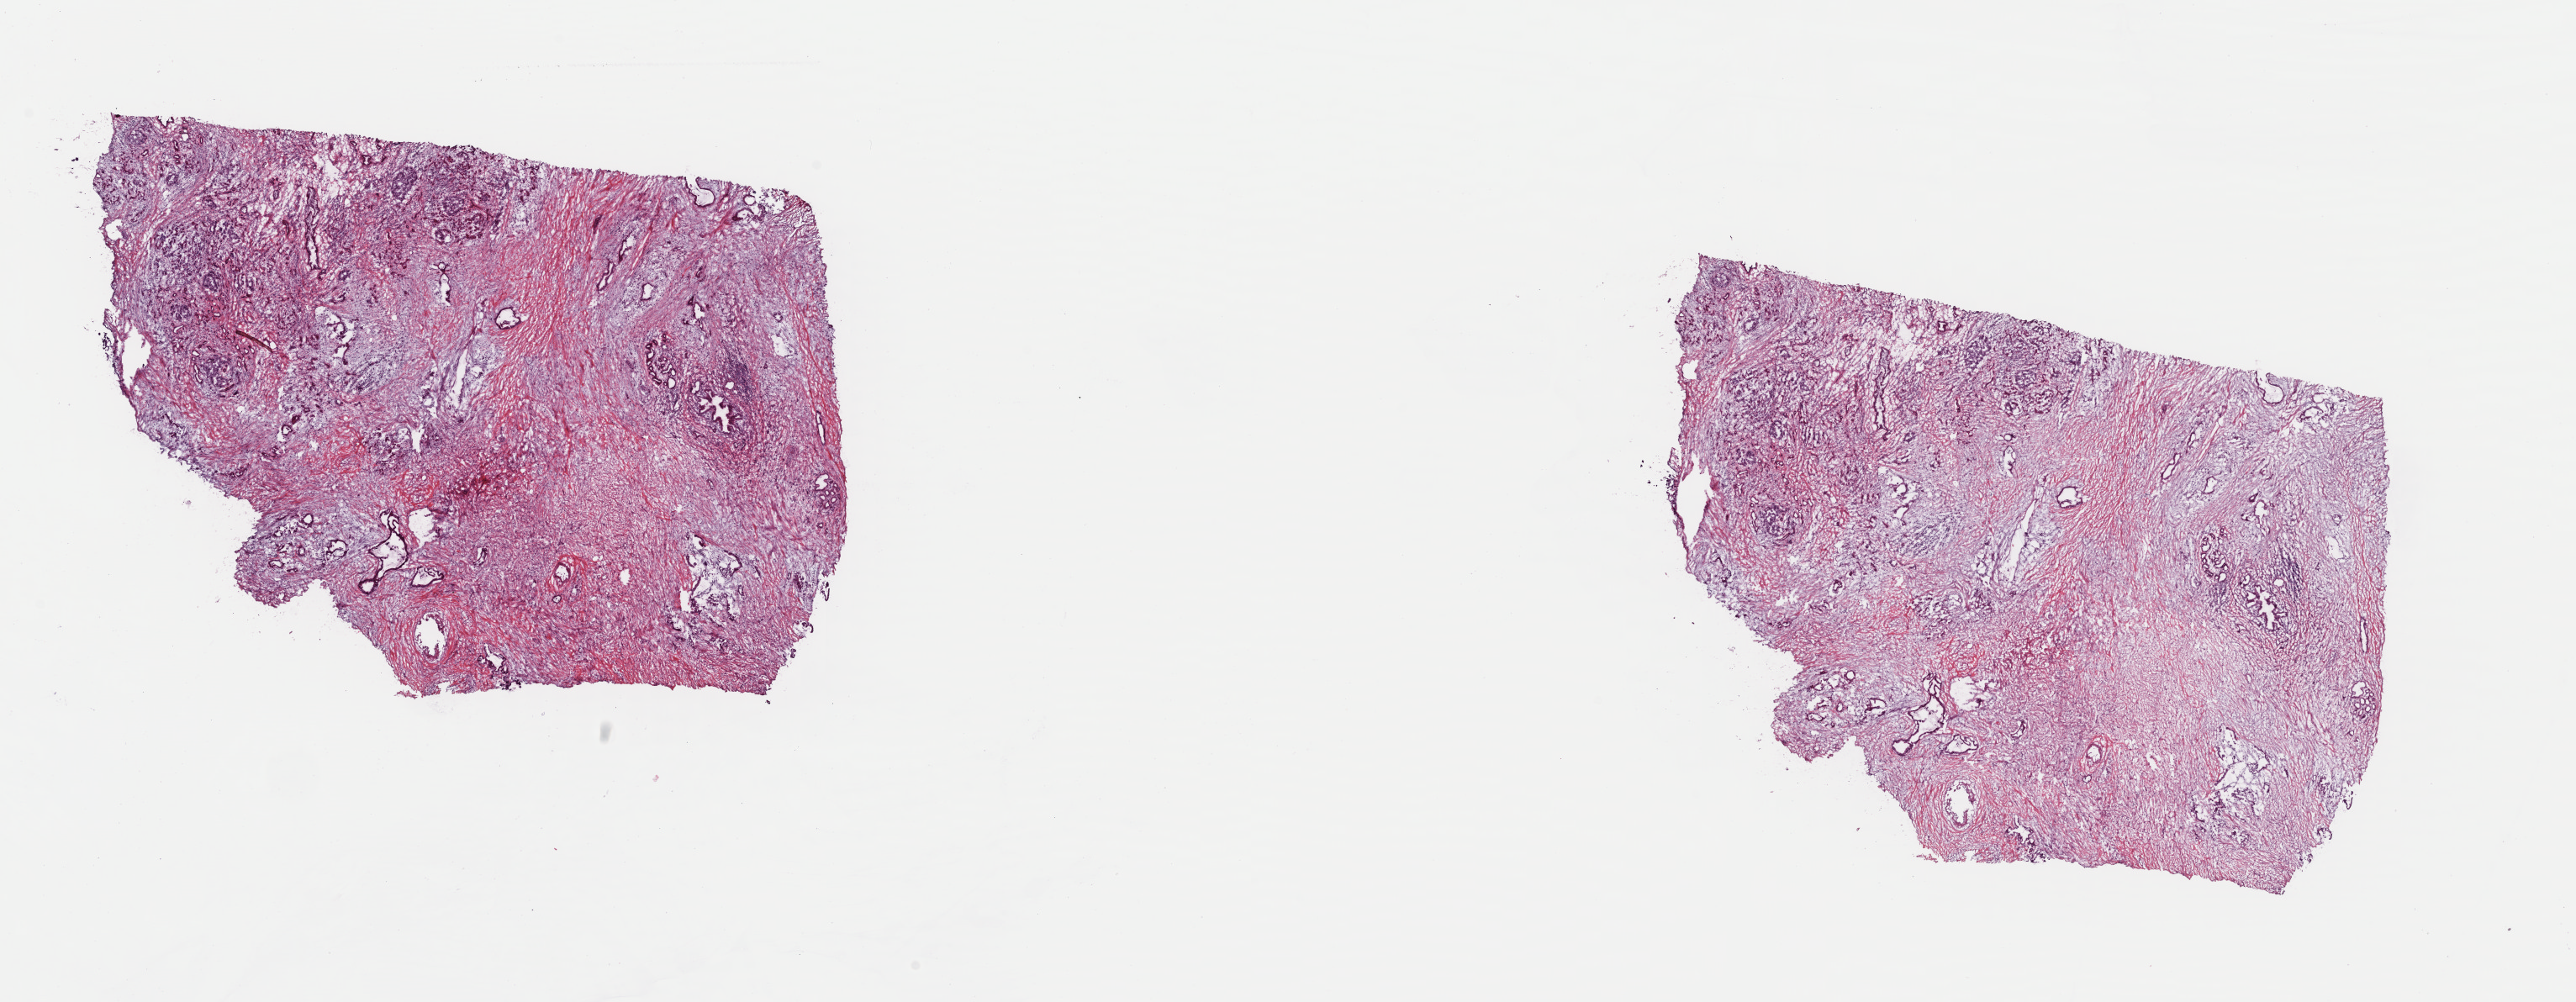
Hematoxylin and eosin (H&E) stained whole-slide image — whole scanned area (about 24.2 x 9.4 mm, from a 40x scan) shown as a low-resolution overview; frozen section; primary tumour sample from the pancreas. Patient: male, age at initial diagnosis 71 years. Histologic grade: G2 (moderately differentiated). Composition of this section per pathologist review: tumour cells 25%, tumour nuclei 50%, normal cells 8%, stromal cells 65%, necrosis 2%. Inflammatory infiltration, as recorded: lymphocyte infiltration 4%, monocyte infiltration 3%, neutrophil infiltration 2%.
Diagnosis: Infiltrating duct carcinoma, NOS (head of pancreas). Lymph nodes positive (case pathology): 3 of 12 examined. TNM: T3 N1 M0. AJCC pathologic stage: IIB.